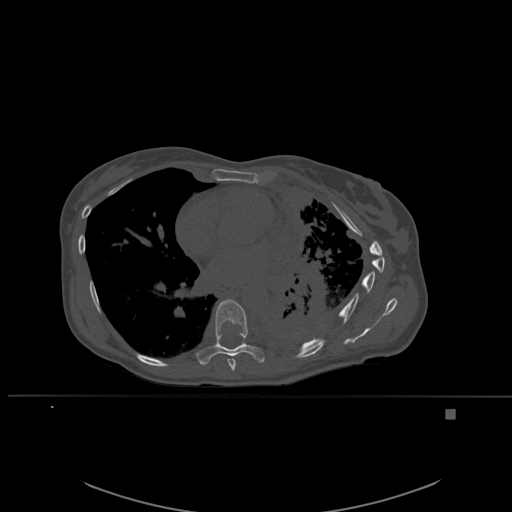
CT including the spine, one axial slice. Slice 352 of 537 in the series (ordered by position). Bone window (W 1800 / L 400 HU). 1.5 mm slice thickness. 512 × 512 image matrix, field of view 440 × 440 mm. Female patient, age 45 years. From the clinical record (not read from this slice): primary cancer: lung.
Structures marked on this image (semi-automatic segmentation, software-assisted and operator-edited):
- T7 vertebra: bounding box (x1, y1, x2, y2) in pixels: (227, 359, 236, 372)
- T8 vertebra: (196, 299, 265, 365)